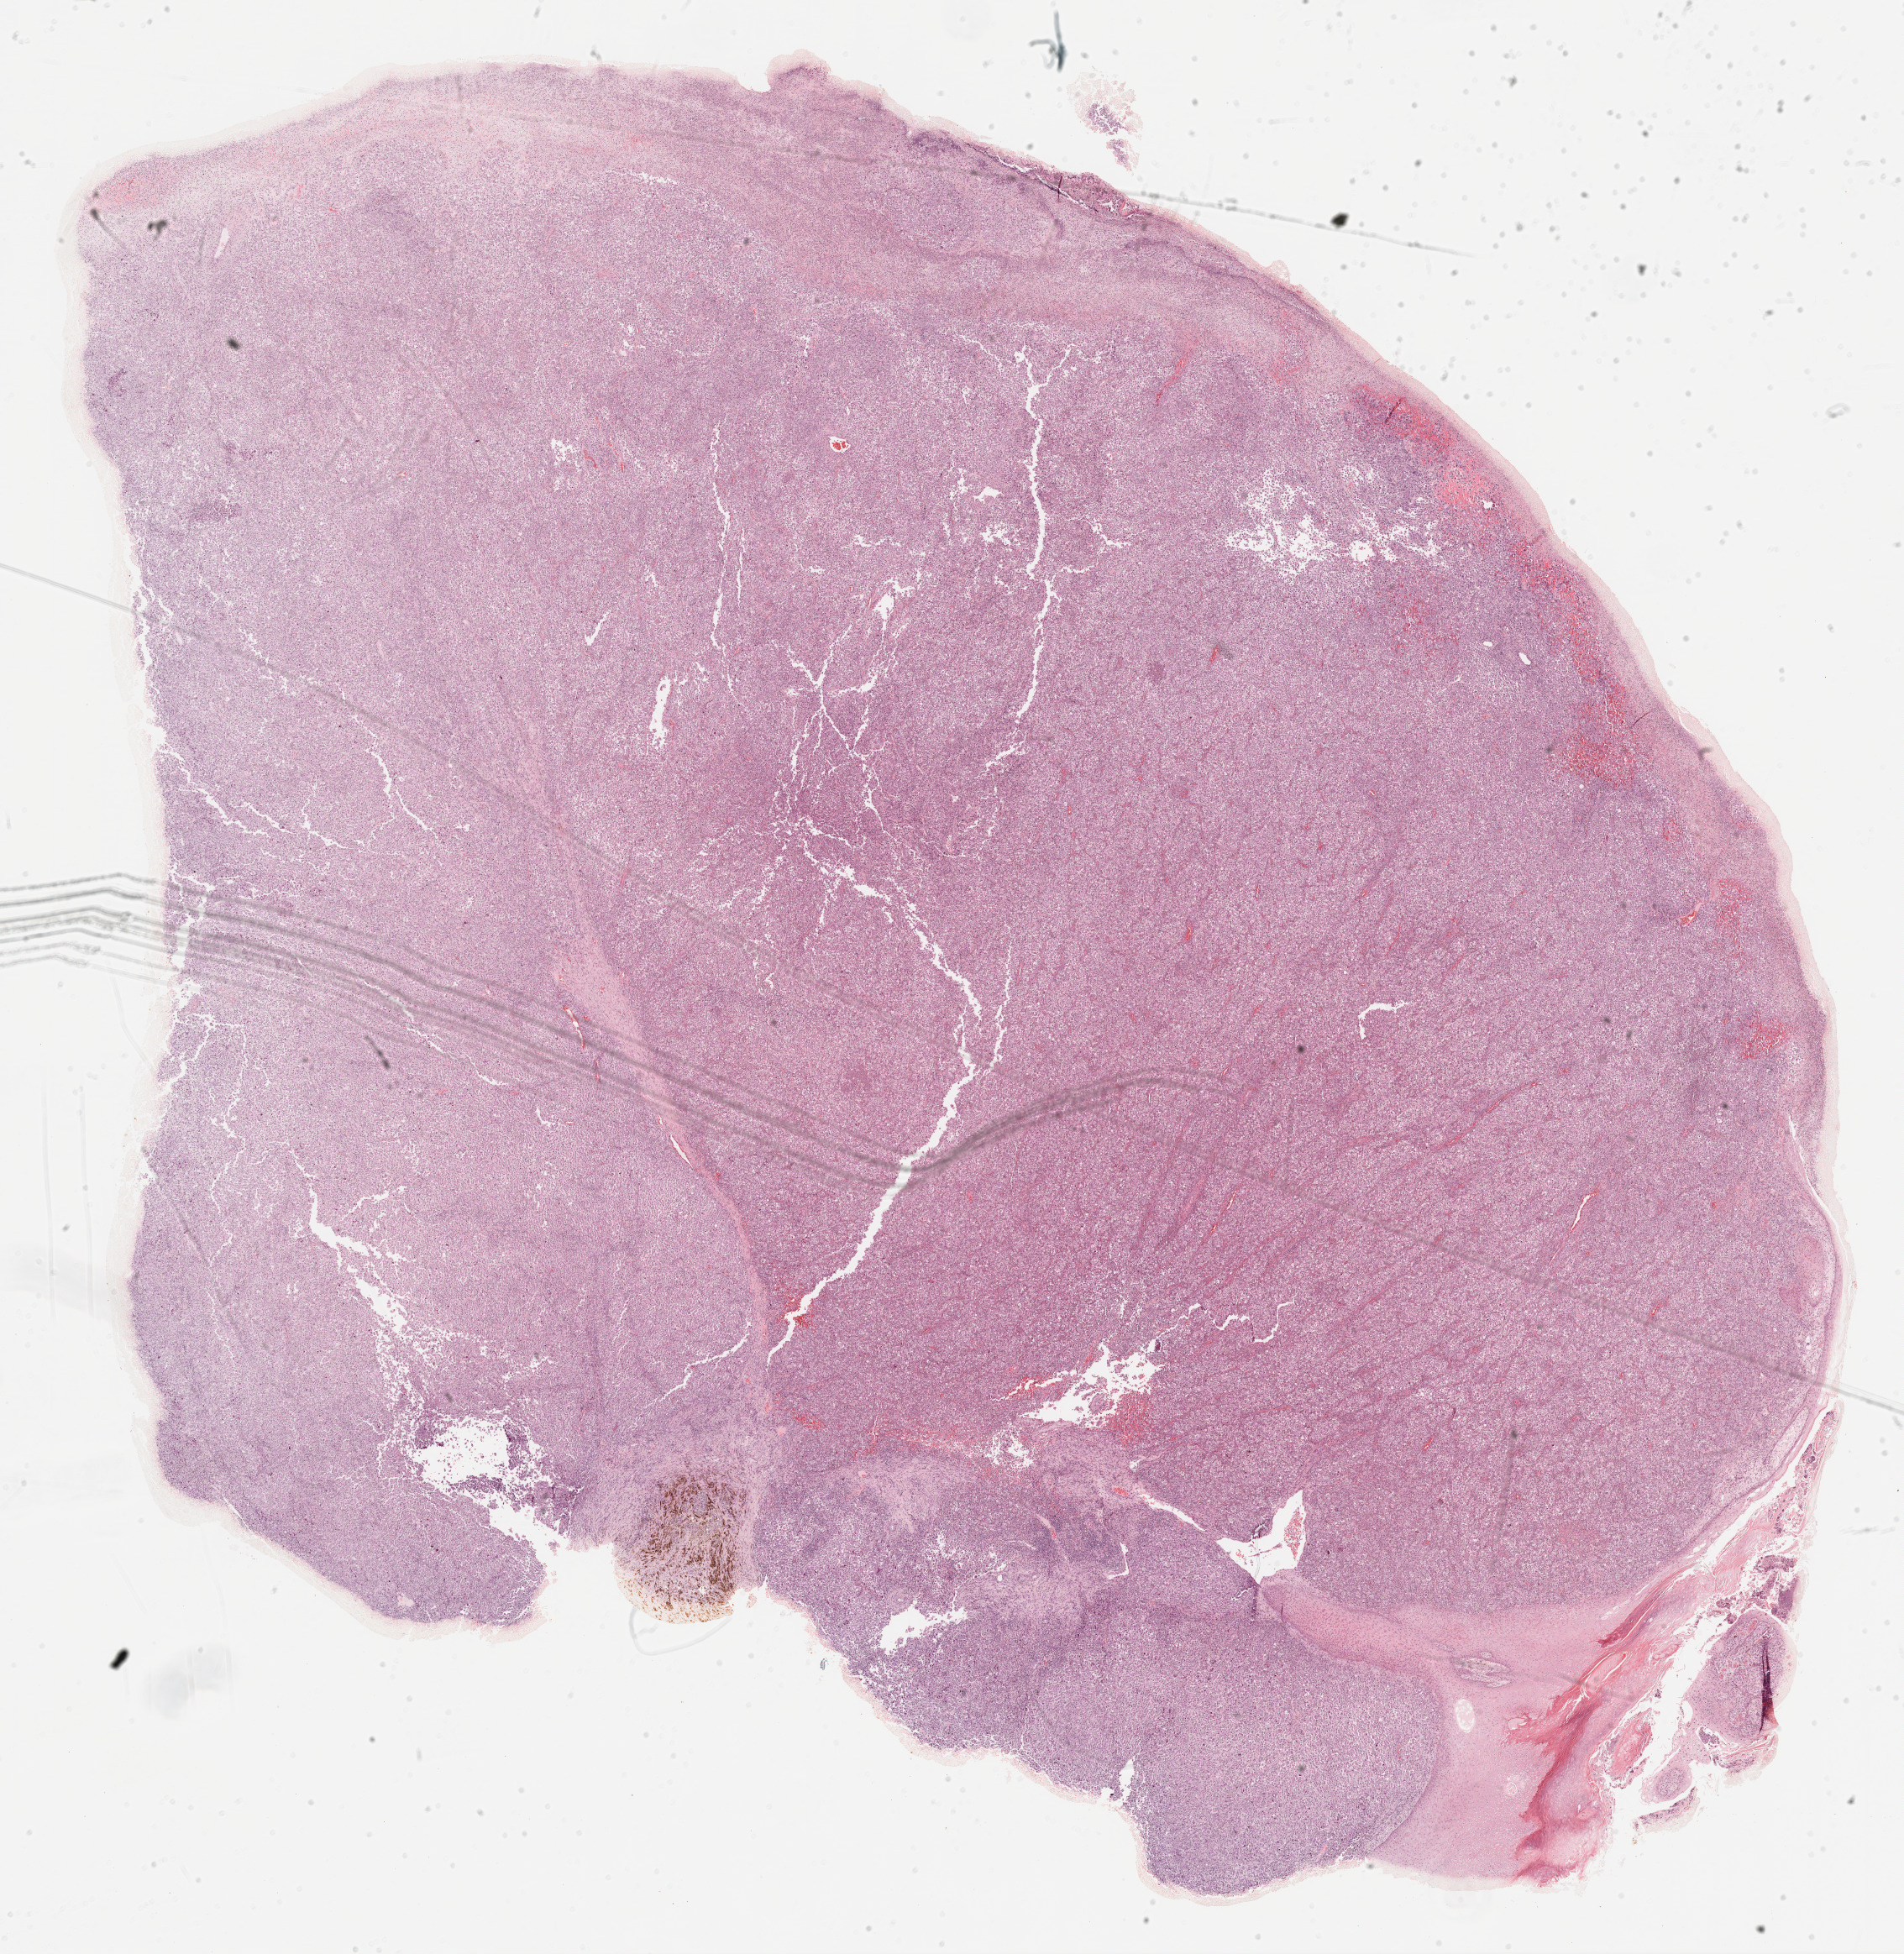
H&E-stained whole-slide image, shown as a low-resolution overview of the whole scanned area (about 18.3 x 18.8 mm), FFPE section, metastatic tumour sample, sampled site not recorded. Patient: male, age at initial diagnosis 55 years.
This section: metastatic tumour tissue. Patient diagnosis: Malignant melanoma, NOS.